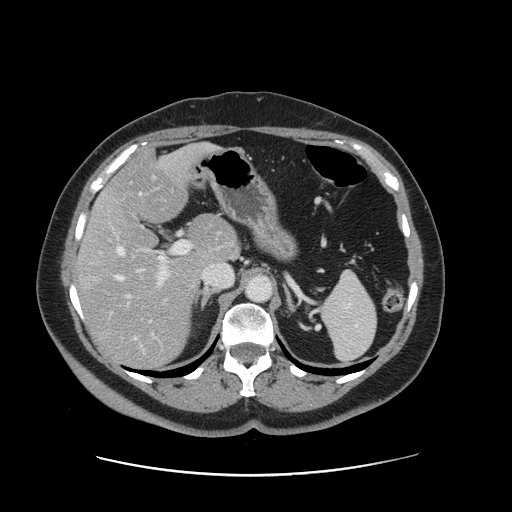
Contrast-enhanced abdominal CT, one axial slice. Slice 90 of 161 in the series (ordered by position). 120 kVp. Soft-tissue window (W 400 / L 40 HU). 2.5 mm slice thickness. 512 × 512 image matrix, field of view 398 × 398 mm. Female patient, age 62 years. Case-level facts recorded for this patient, not image findings: diagnosis: colorectal cancer liver metastases, imaged before liver resection; multiple liver metastases: no; largest metastasis: 2.5 cm; disease in both lobes: no.
Outlined on this slice (manually delineated by an expert):
- hepatic veins: bounding box <117,192,144,339> (left, top, right, bottom; pixels)
- liver: <80,145,237,367>
- planned liver remnant (the part of the liver to remain after resection): <107,144,237,265>
- portal vein (with intrahepatic branches): <121,241,191,339>